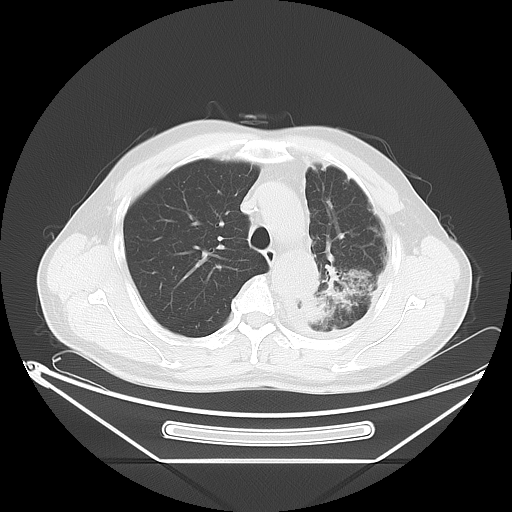
Chest CT, one axial slice. Slice 45 of 63 in the series (ordered by position). Reconstruction kernel LUNG. Lung window (W 1500 / L -600 HU). 5 mm slice thickness. 512 × 512 image matrix. Patient: male, 60 years. From the clinical record (not read from this slice): clinical TNM (as recorded): T4 N1 M1.
Structures marked on this image (bounding box drawn by a radiologist):
- lung tumour (recorded histology: adenocarcinoma): box from (x=289, y=290) to (x=342, y=336) px